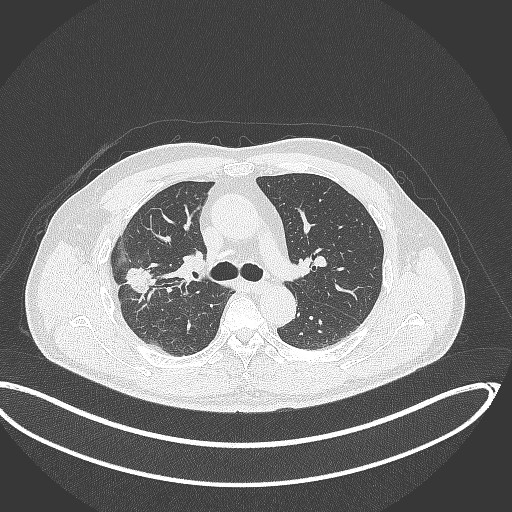
Chest CT, one axial slice. Position 222 of 391 along the scan axis. 120 kVp. Lung window (W 1500 / L -600 HU). 1 mm slice thickness. 512 × 512 image matrix, field of view 439 × 439 mm. Male patient, age 63 years. Case-level facts recorded for this patient, not image findings: clinical TNM (as recorded): T1c N0 M0; histopathological grade: G2-3.
Outlined on this slice (rectangle marked by the reading radiologist):
- lung tumour (recorded histology: adenocarcinoma): bounding box [x1, y1, x2, y2] px = [119, 256, 162, 303]